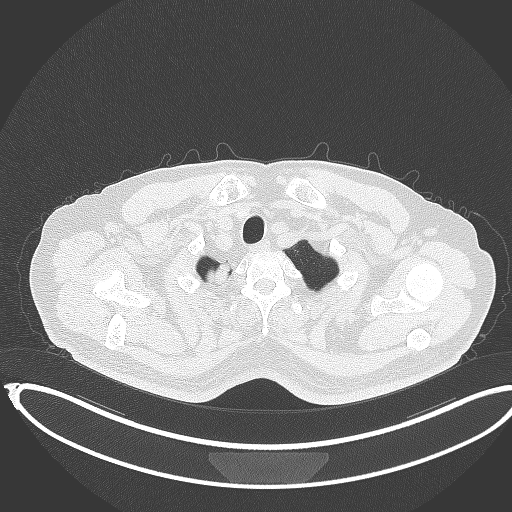
Chest CT, one axial slice. Position 345 of 403 along the scan axis. 120 kVp. Lung window (W 1500 / L -600 HU). 1 mm slice thickness. 512 × 512 image matrix, field of view 436 × 436 mm. Male patient, age 68 years. From the clinical record (not read from this slice): clinical TNM (as recorded): T2a N0 M0.
Structures marked on this image (bounding box drawn by a radiologist):
- lung tumour (recorded histology: adenocarcinoma): box from (x=206, y=260) to (x=237, y=290) px